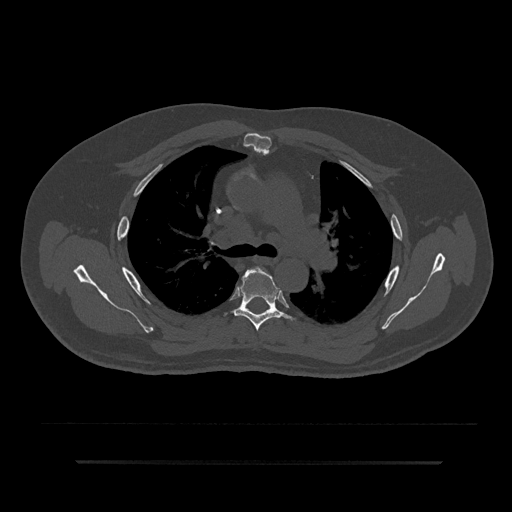
CT including the spine, one axial slice; slice 576 of 797 in the series (ordered by position); reconstruction kernel Br40s/3; 120 kVp; bone window (W 1800 / L 400 HU); 0.5 mm slice thickness; 512 × 512 image matrix. Male patient, age 59 years. Case-level facts recorded for this patient, not image findings: primary cancer: bile ducts; vertebrae with lytic lesions (as recorded): T10.
Outlined on this slice (semi-automatic segmentation, software-assisted and operator-edited):
- T4 vertebra: bounding box [x1, y1, x2, y2] px = [253, 266, 262, 270]
- T5 vertebra: [233, 268, 292, 331]